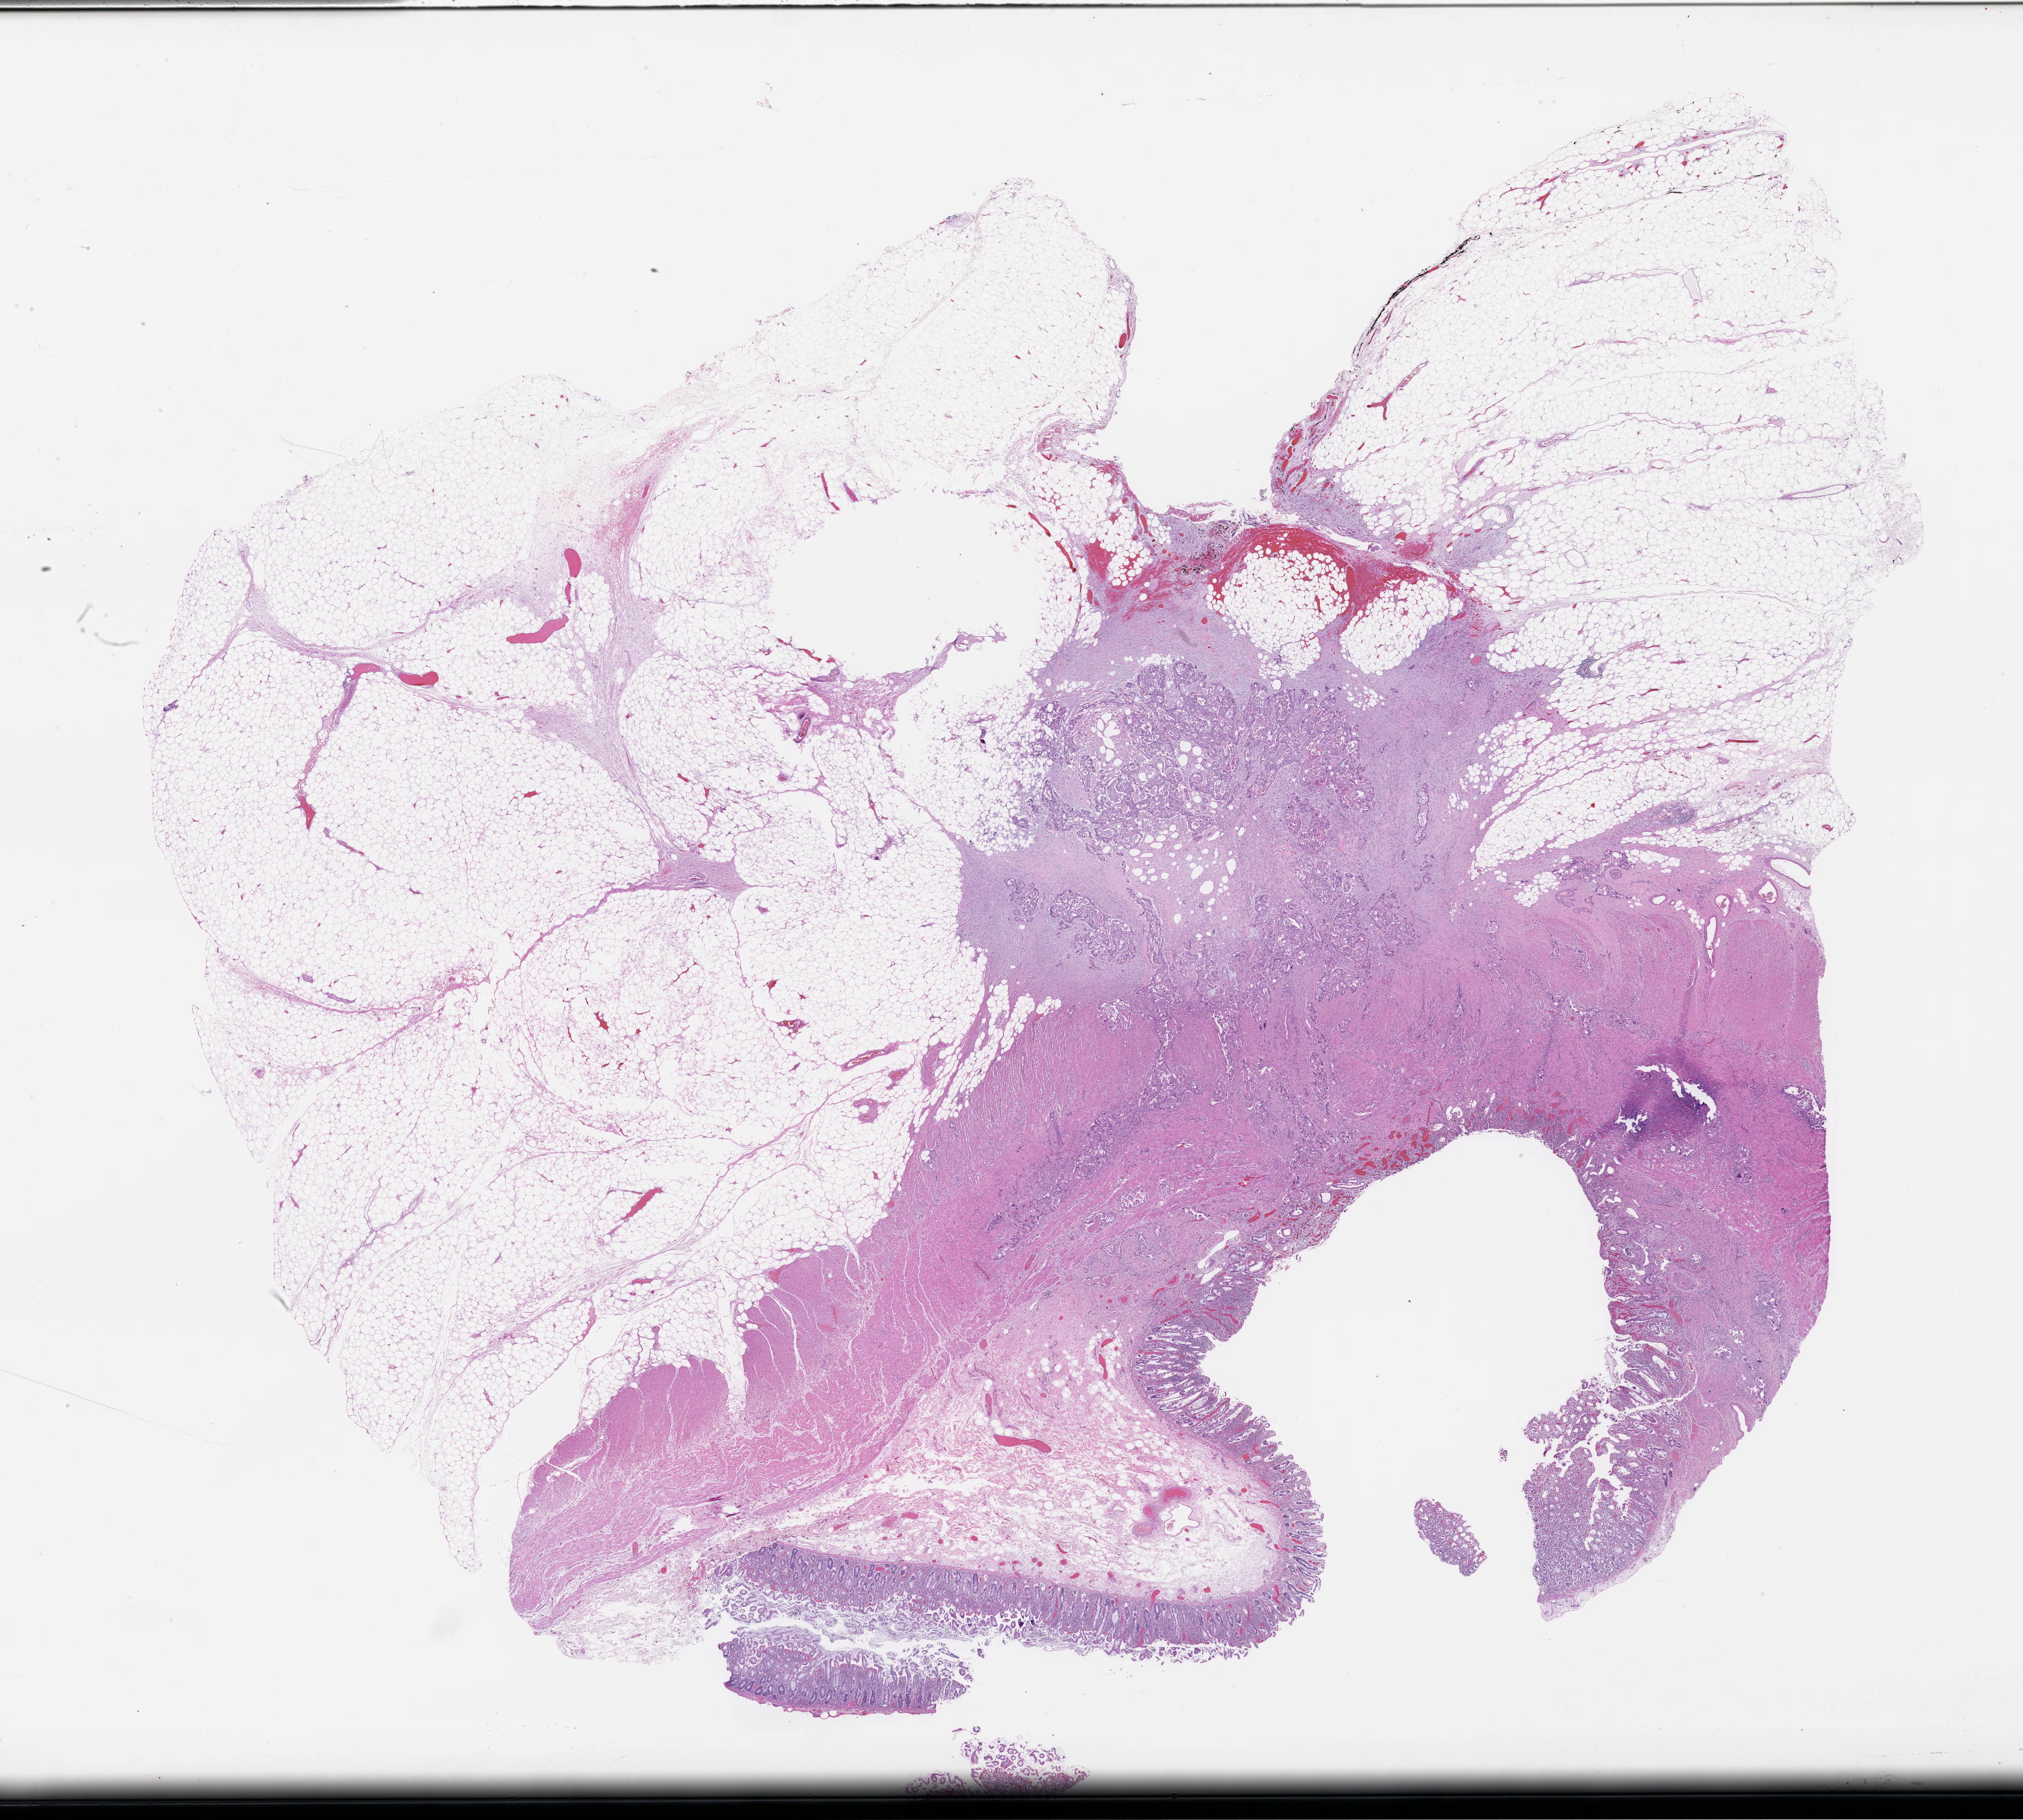
Whole-slide image, haematoxylin and eosin stain, shown as a low-resolution overview of the whole scanned area (about 27.1 x 24.4 mm); FFPE section; site: colon; archival tissue. Female patient.
- this section: primary tumor
- diagnosis: Colorectal Carcinoma